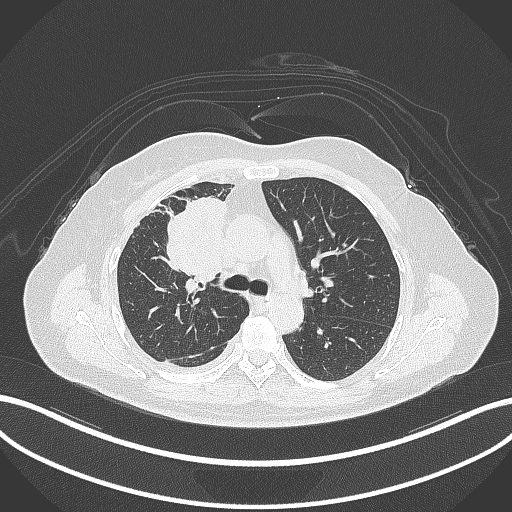
Chest CT, one axial slice; position 185 of 305 along the scan axis; lung window (W 1500 / L -600 HU); 512 × 512 image matrix. Female patient, age 52 years. Case-level facts recorded for this patient, not image findings: clinical TNM (as recorded): T3 N1 M1.
Annotated regions visible in this slice (rectangle marked by the reading radiologist):
- lung tumour (recorded histology: adenocarcinoma): bounding box [x1, y1, x2, y2] px = [165, 198, 227, 287]